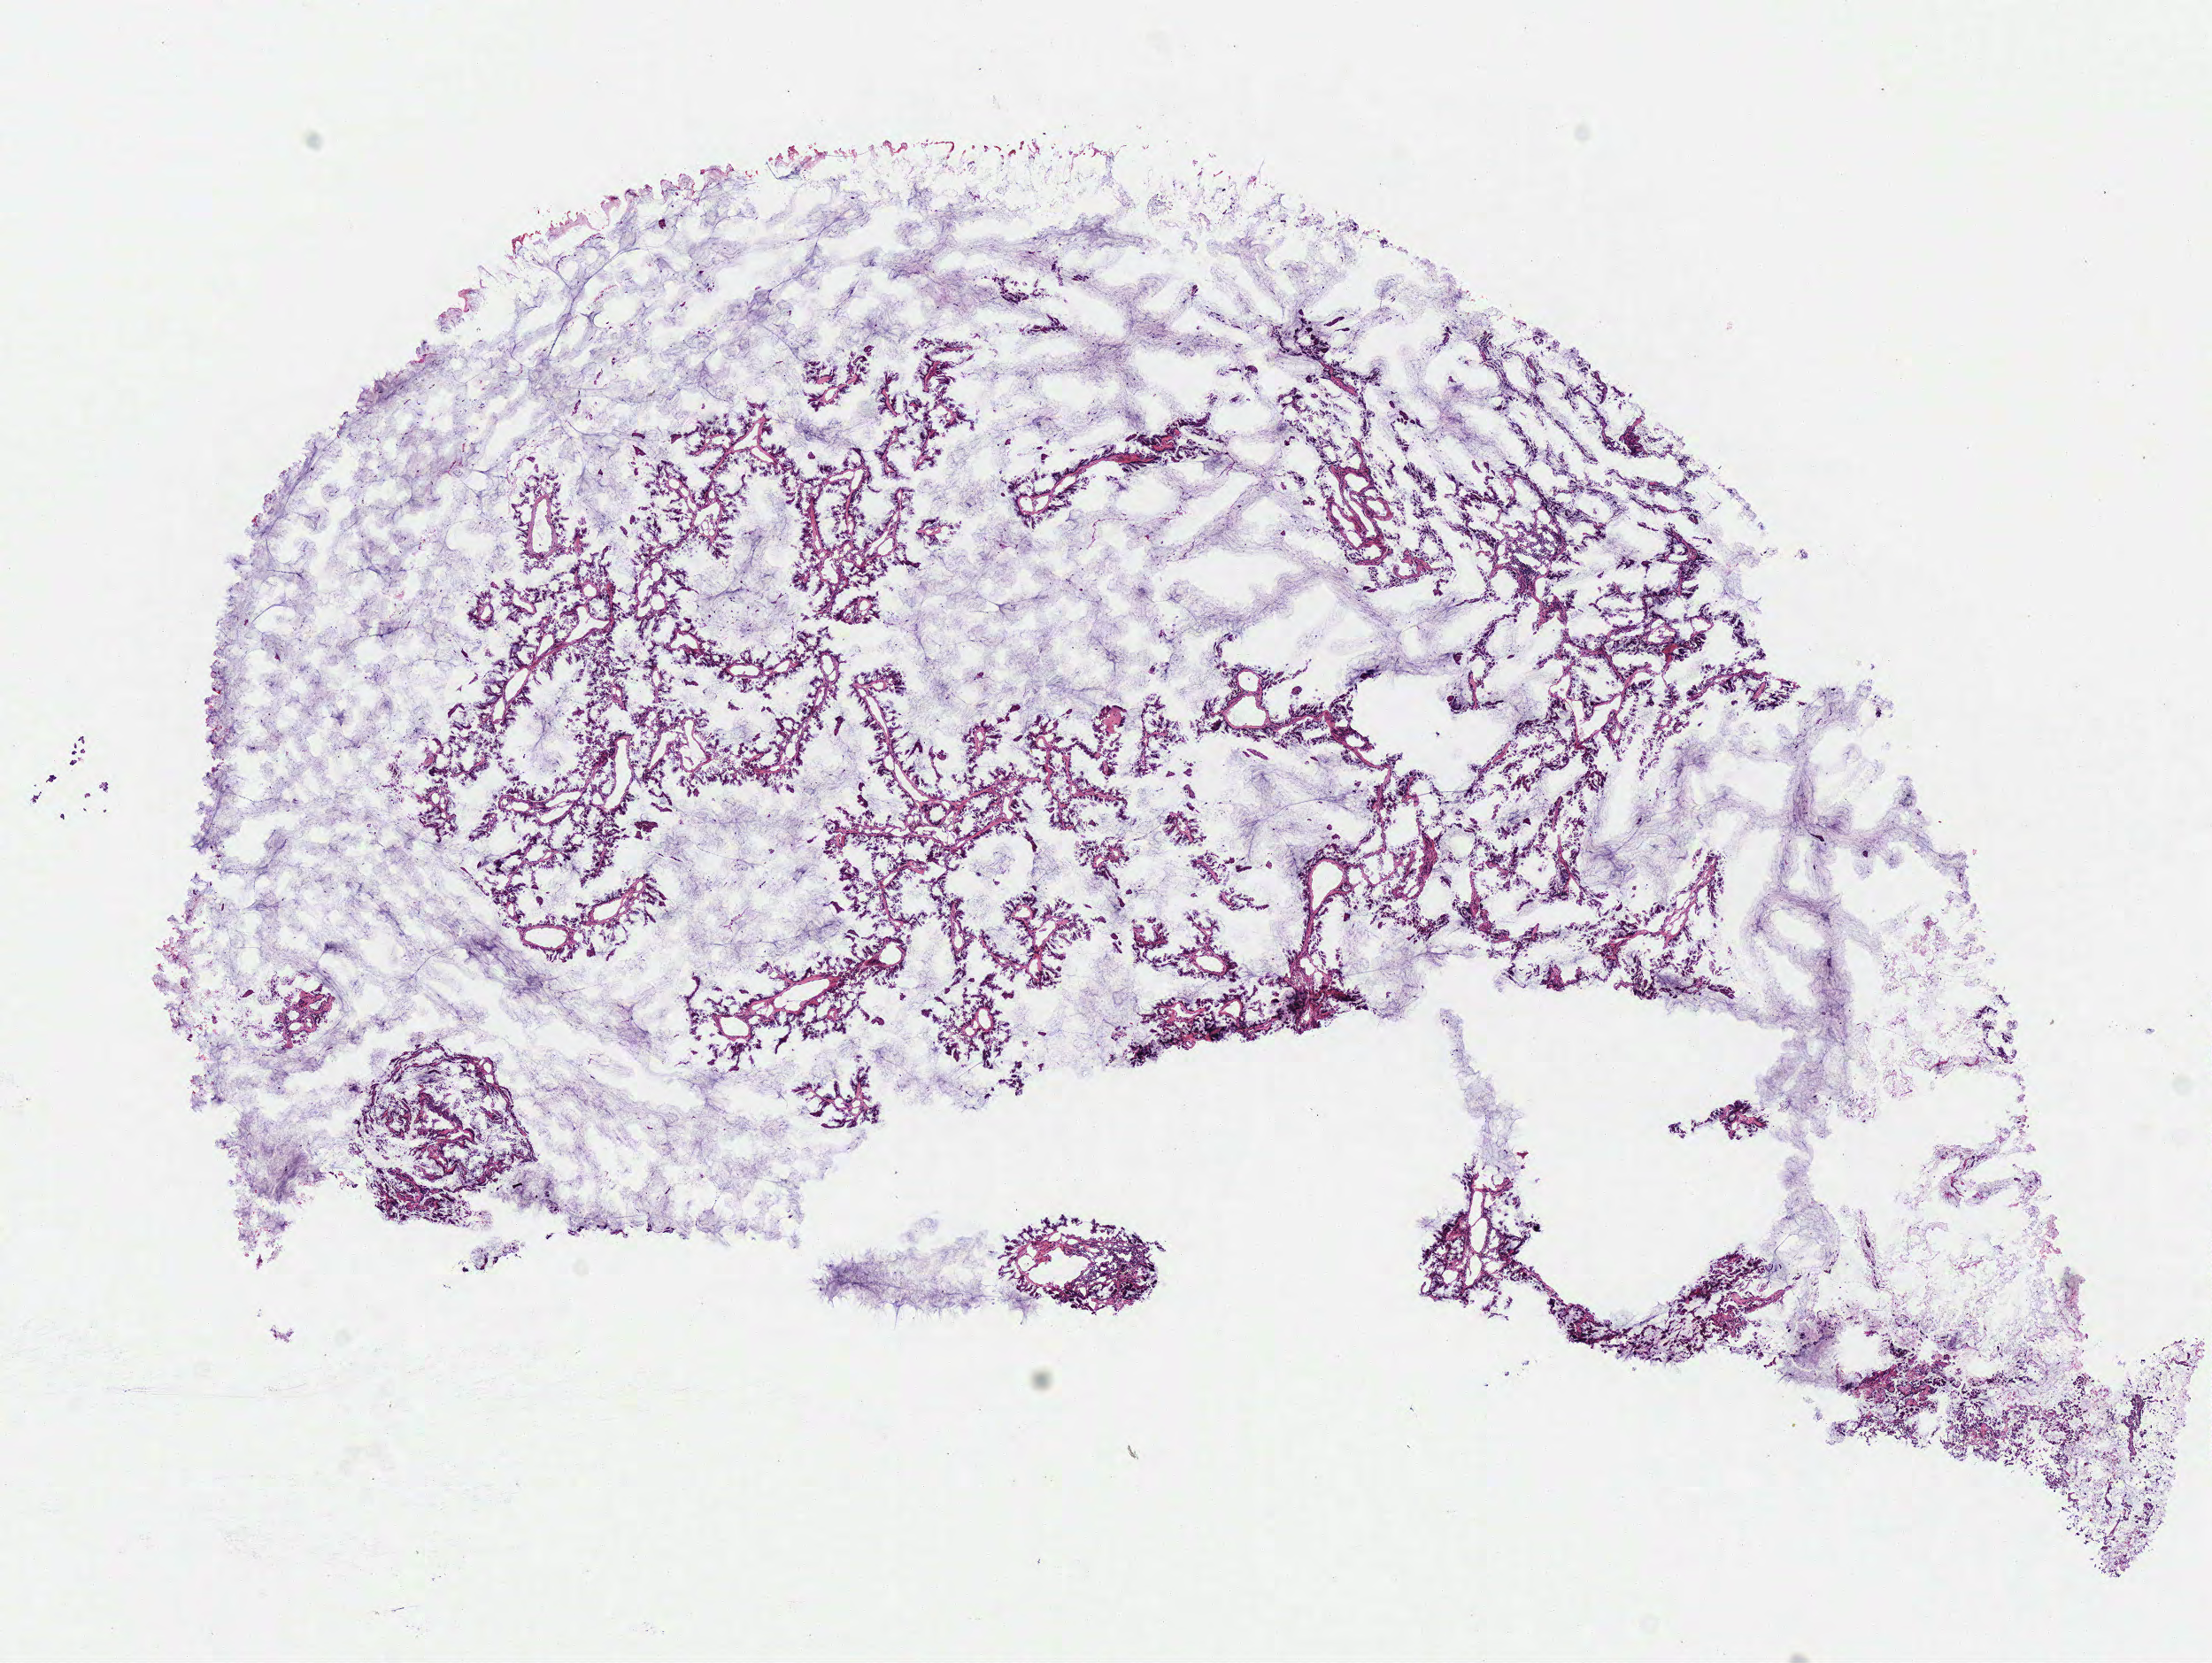
Digitized Hematoxylin and eosin (H&E) stained tissue section (whole slide), a low-resolution overview of the entire scanned area, about 9.8 x 7.4 mm (from a 40x scan), frozen section from the bottom of the tissue portion, sample: primary tumour, lung. Patient: male, age at initial diagnosis 60 years. Pathologist review of this section (percent, as recorded): tumour cells 85%, tumour nuclei 80%, normal cells 0%, stromal cells 15%, necrosis 0%.
Histologic diagnosis: Adenocarcinoma, NOS (lower lobe, lung). AJCC pathologic stage: IB.